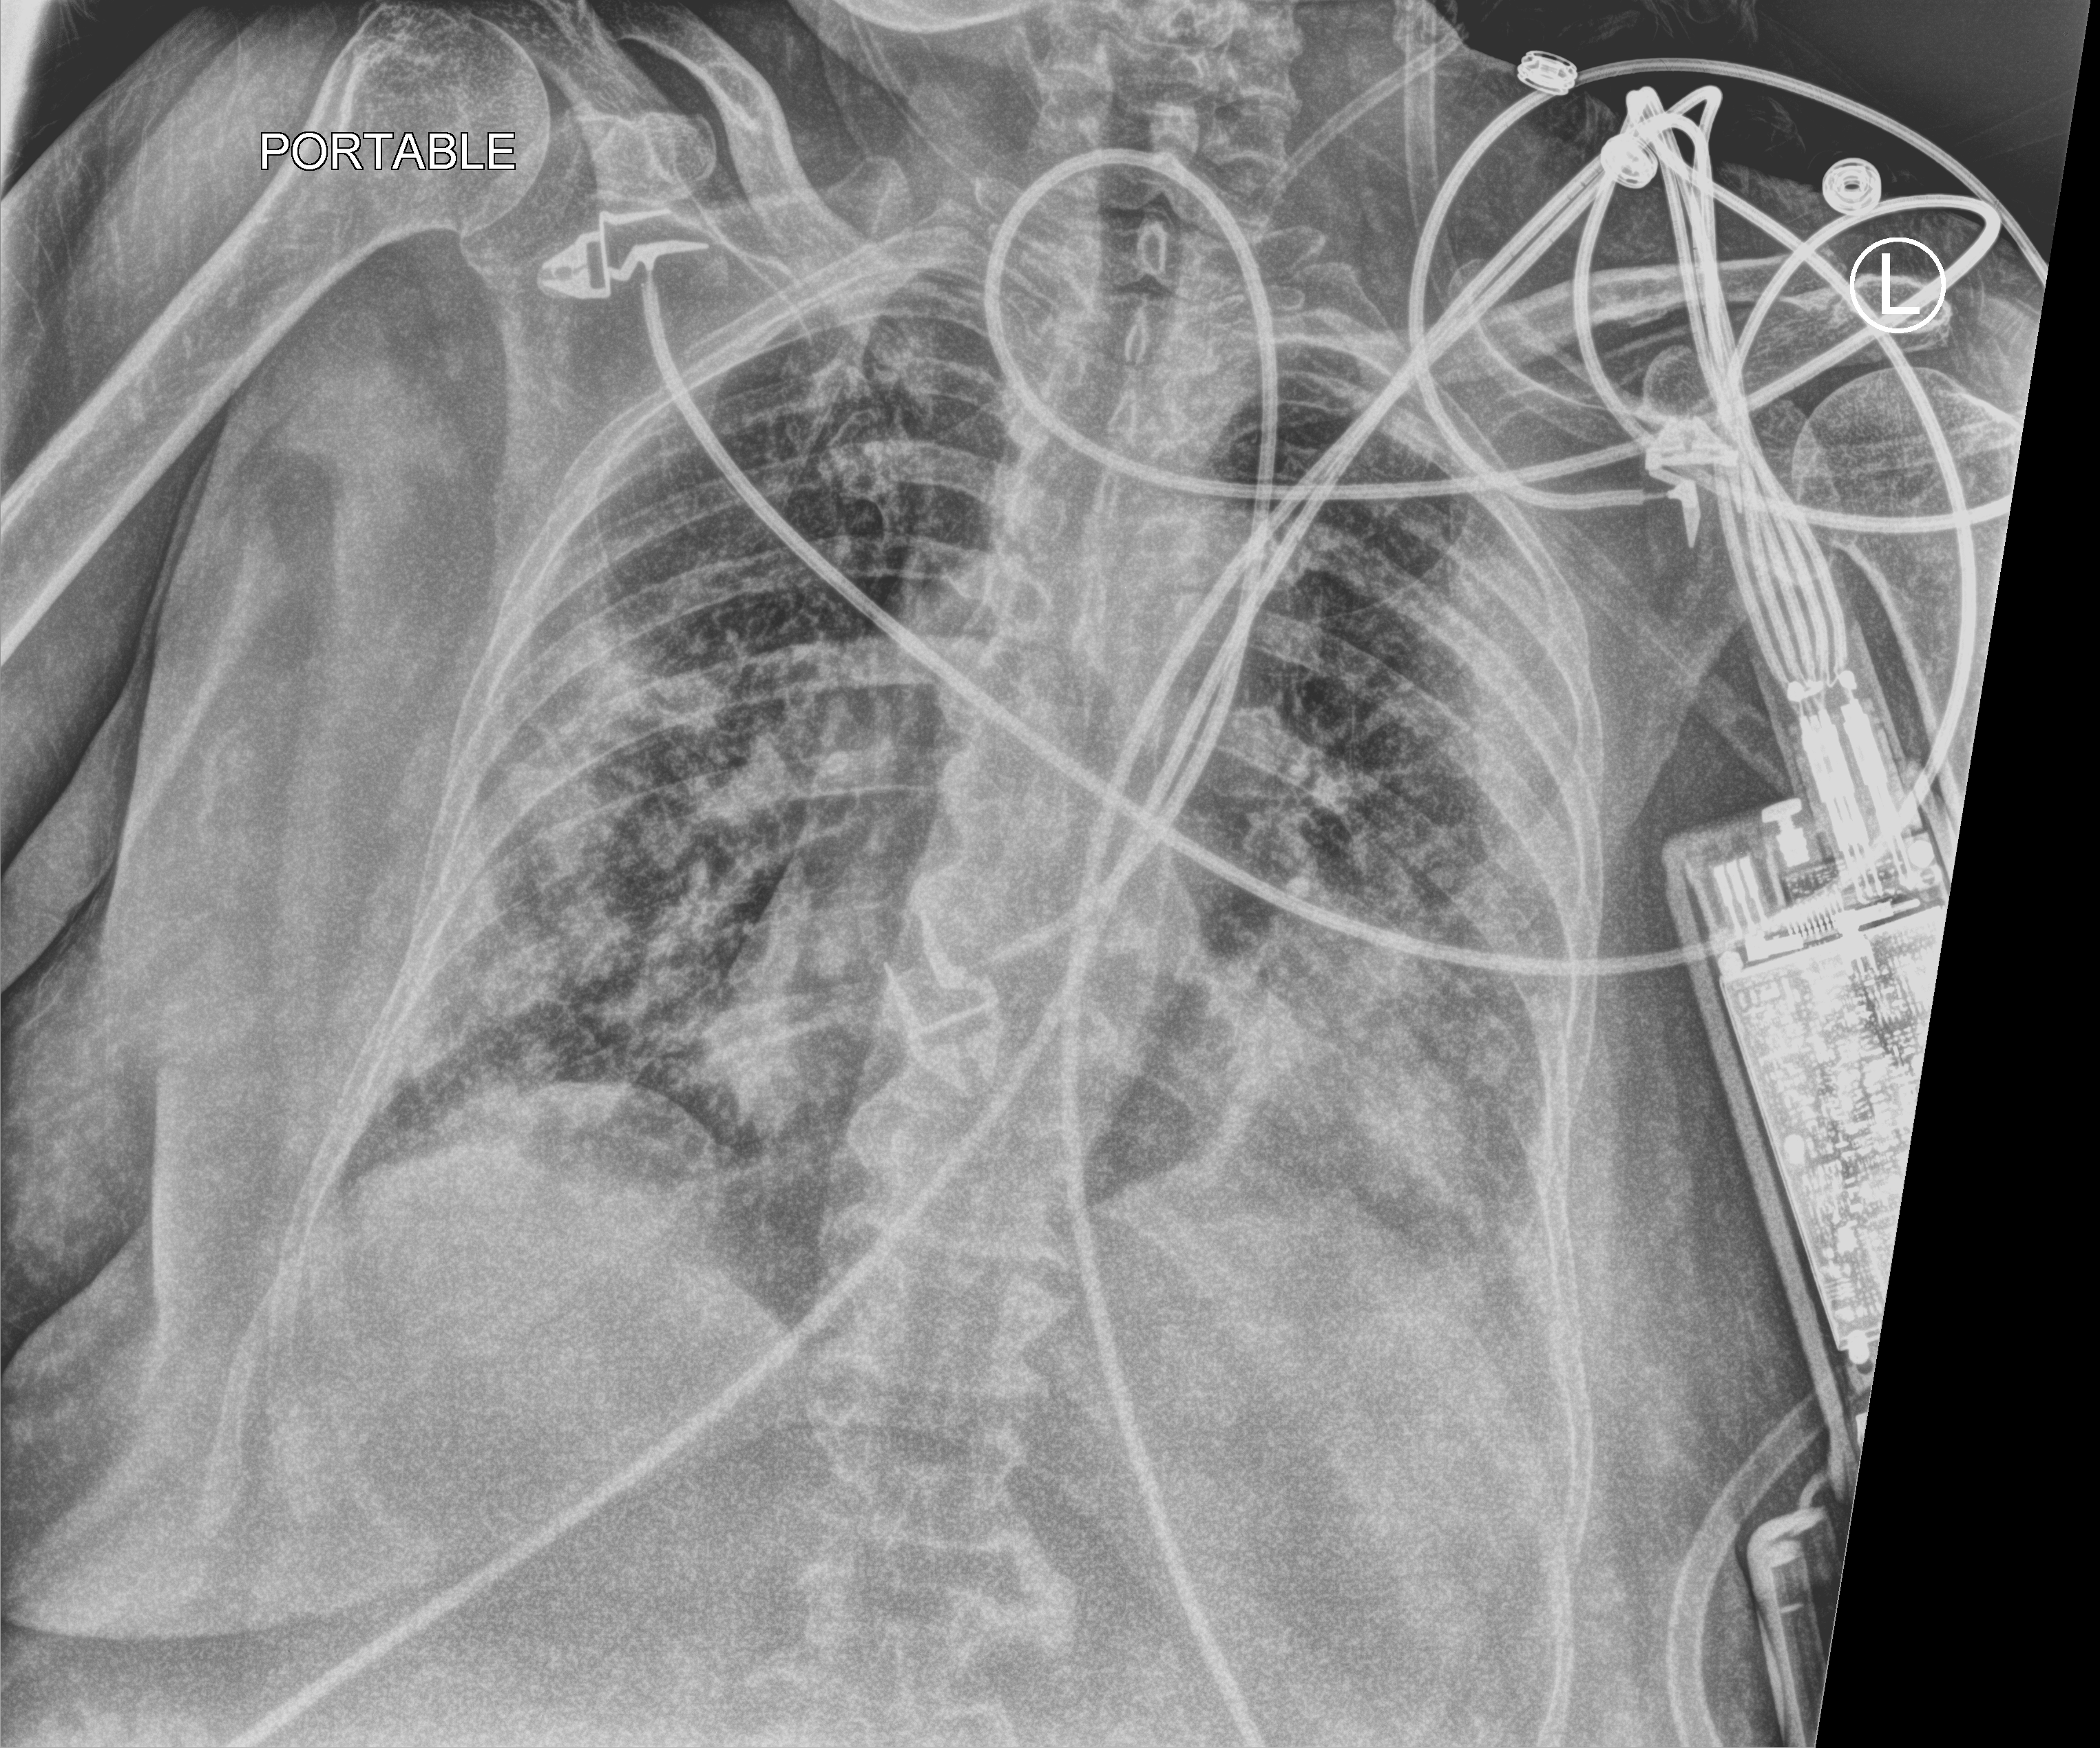
Chest X-ray (portable), anteroposterior (AP) projection. Female patient hospitalised with COVID-19, age 75–90 years.
Hospital-stay facts (about this admission, not read from this image; timing relative to this image not recorded): admitted to intensive care during this hospital stay: yes.